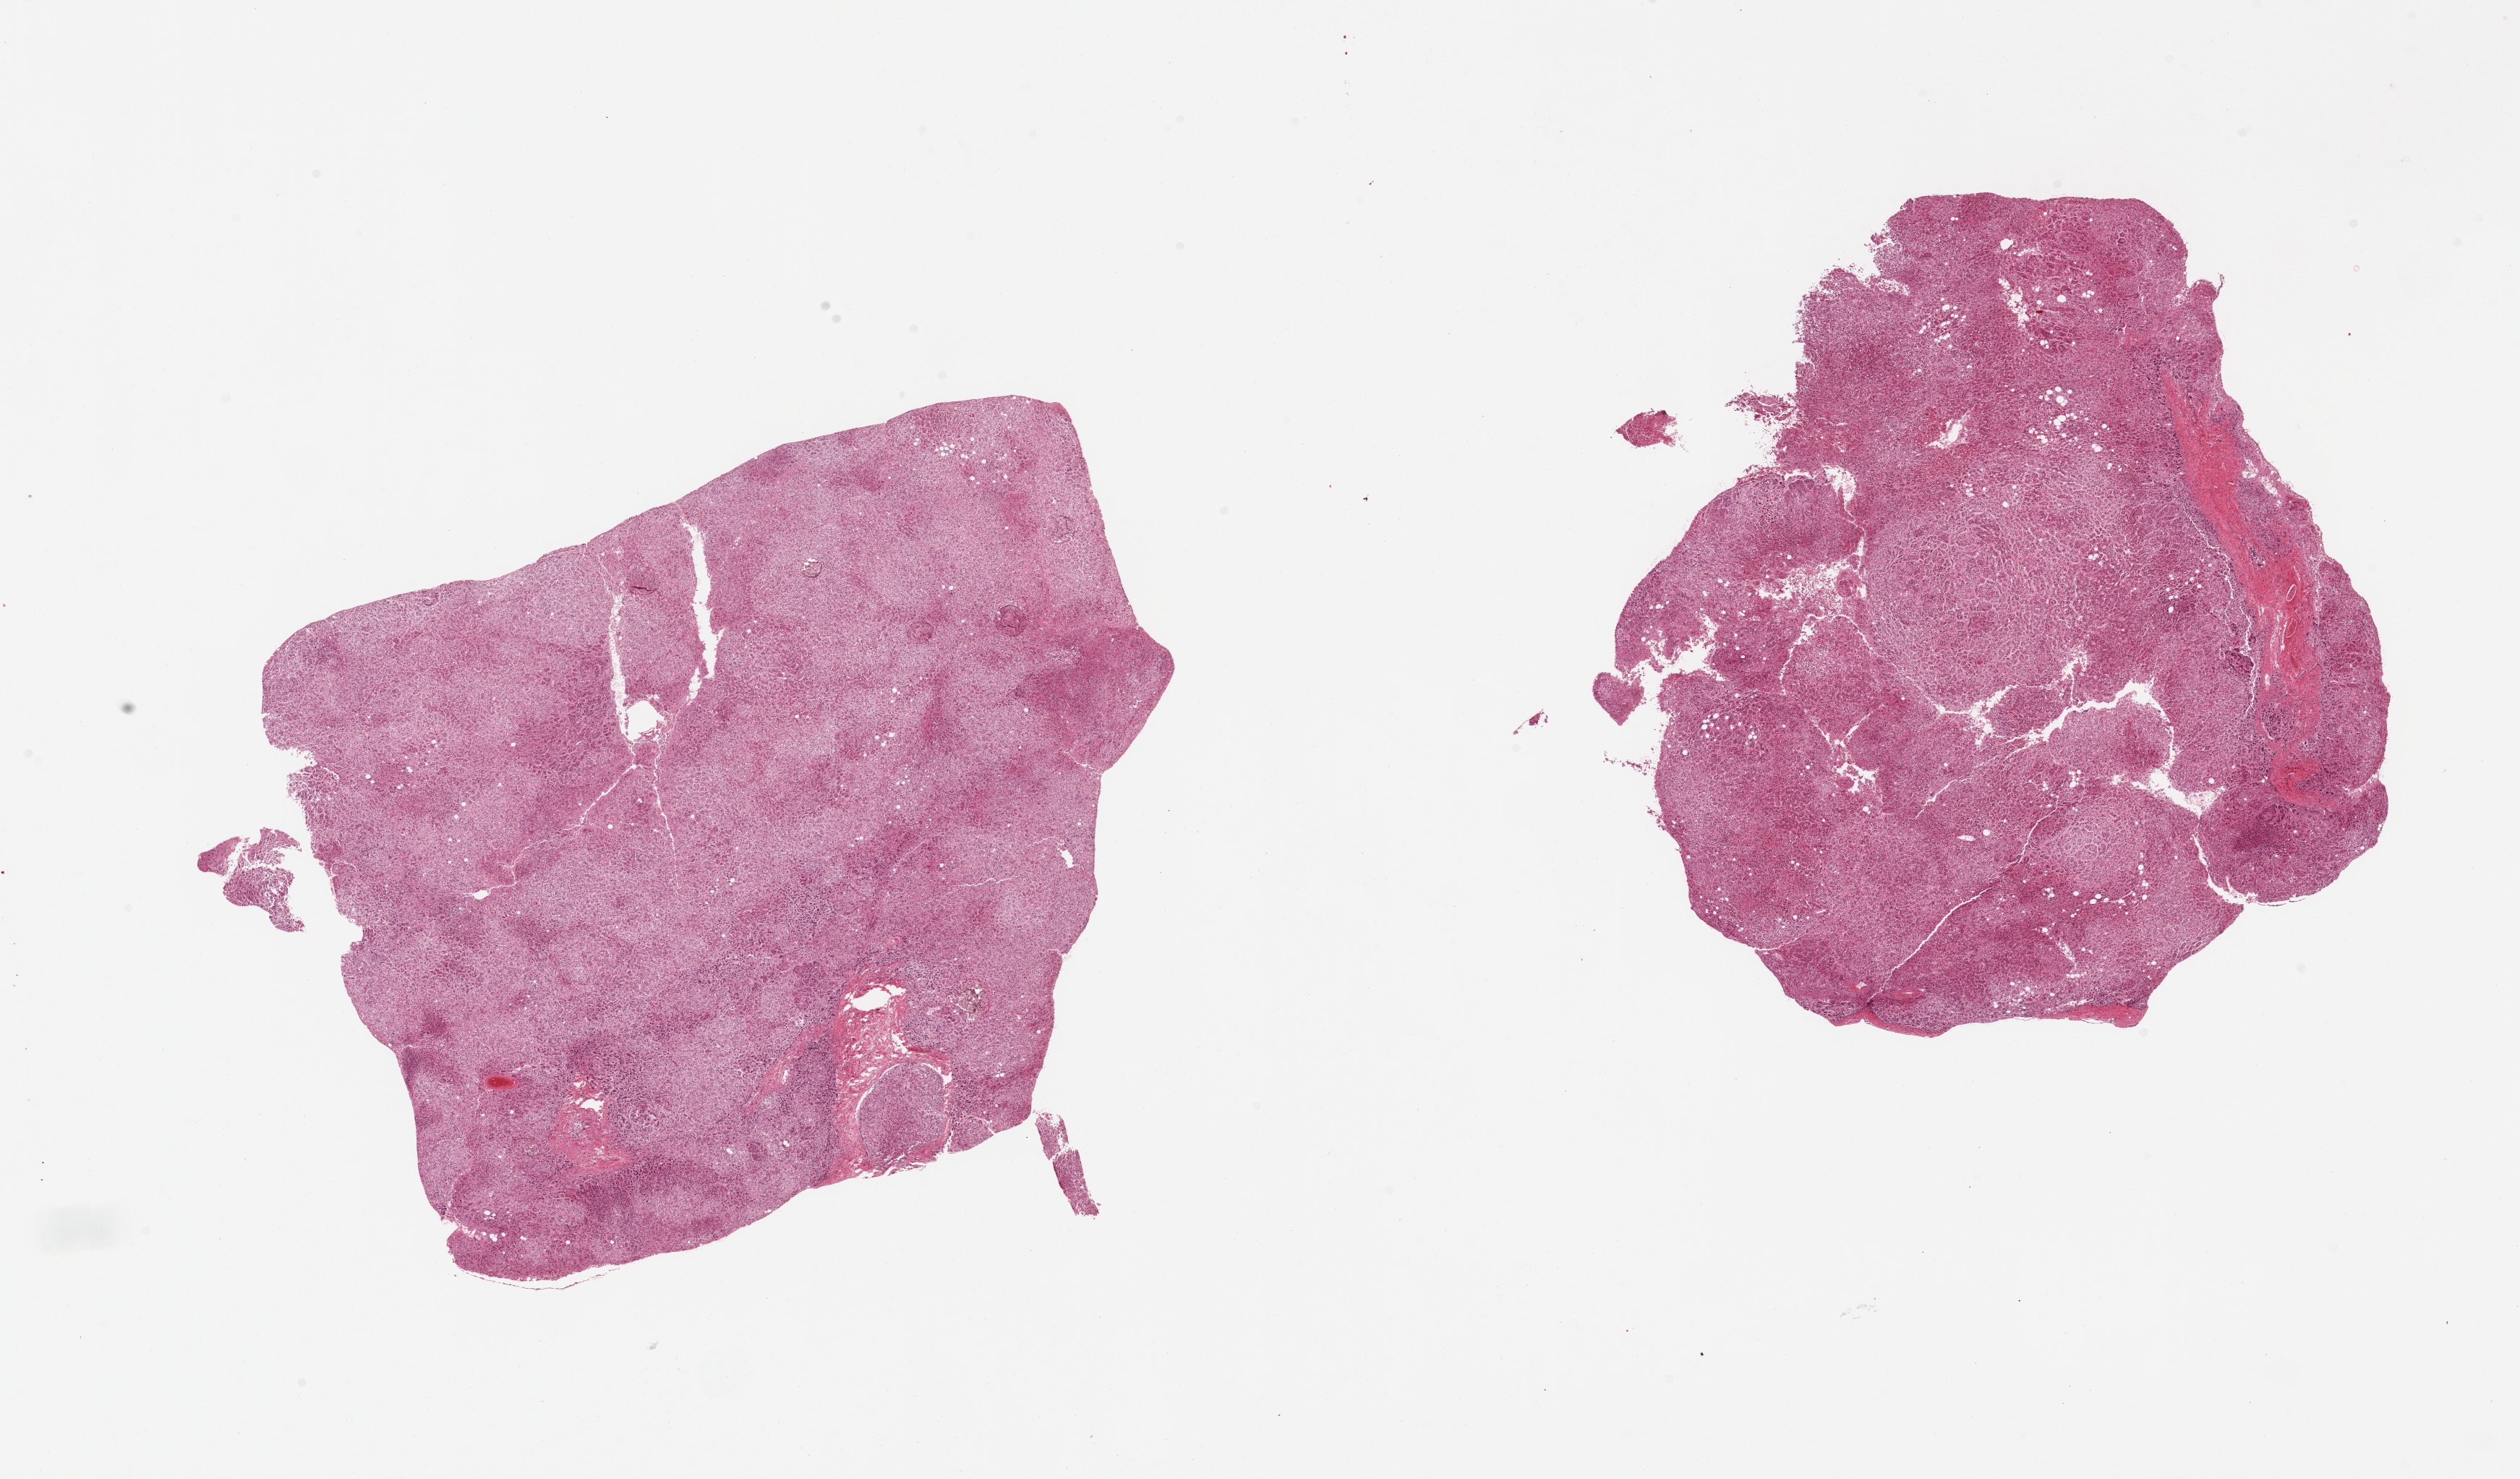
Hematoxylin and eosin (H&E) whole-slide image, brightfield — low-resolution overview of the scanned area, about 27.6 x 16.2 mm (acquisition: 20x scan), PAXgene-fixed paraffin-embedded (PFPE) section, target tissue: adrenal gland, tissue donor sample. Donor sex: female.
Reviewer comment on this tissue sample: 2 pieces; grade 2/3 autolyzed cortex.